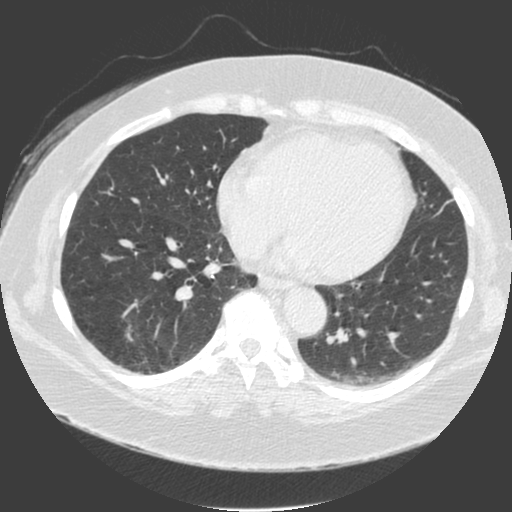
Low-dose screening chest CT, one axial slice; position 71 of 175 along the scan axis; 120 kVp; lung window (W 1500 / L -600 HU); 2 mm slice thickness; 512 × 512 image matrix.
Annotated regions visible in this slice (expert manual segmentation):
- lesion 1 (tumor, lower lobe of right lung): bounding box (x1, y1, x2, y2) in pixels: (127, 333, 132, 341)